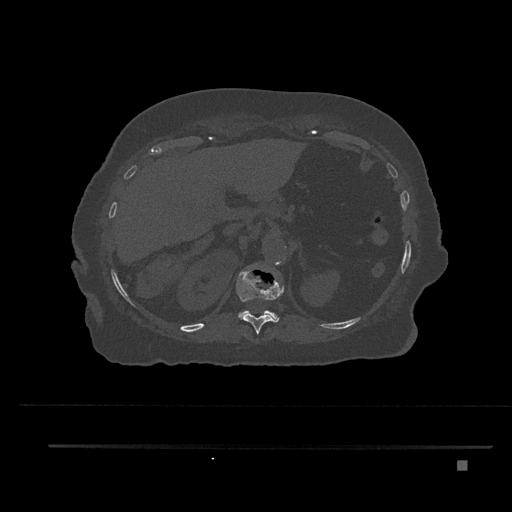
CT including the spine, one axial slice. 120 kVp. Bone window (W 1800 / L 400 HU). 0.5 mm slice thickness. 512 × 512 image matrix. Female patient, age 76 years. From the clinical record (not read from this slice): primary cancer: lung.
Annotated regions visible in this slice (semi-automatically segmented with operator editing):
- T11 vertebra: box from (x=236, y=269) to (x=284, y=334) px
- T12 vertebra: (x=238, y=310)–(x=279, y=321)